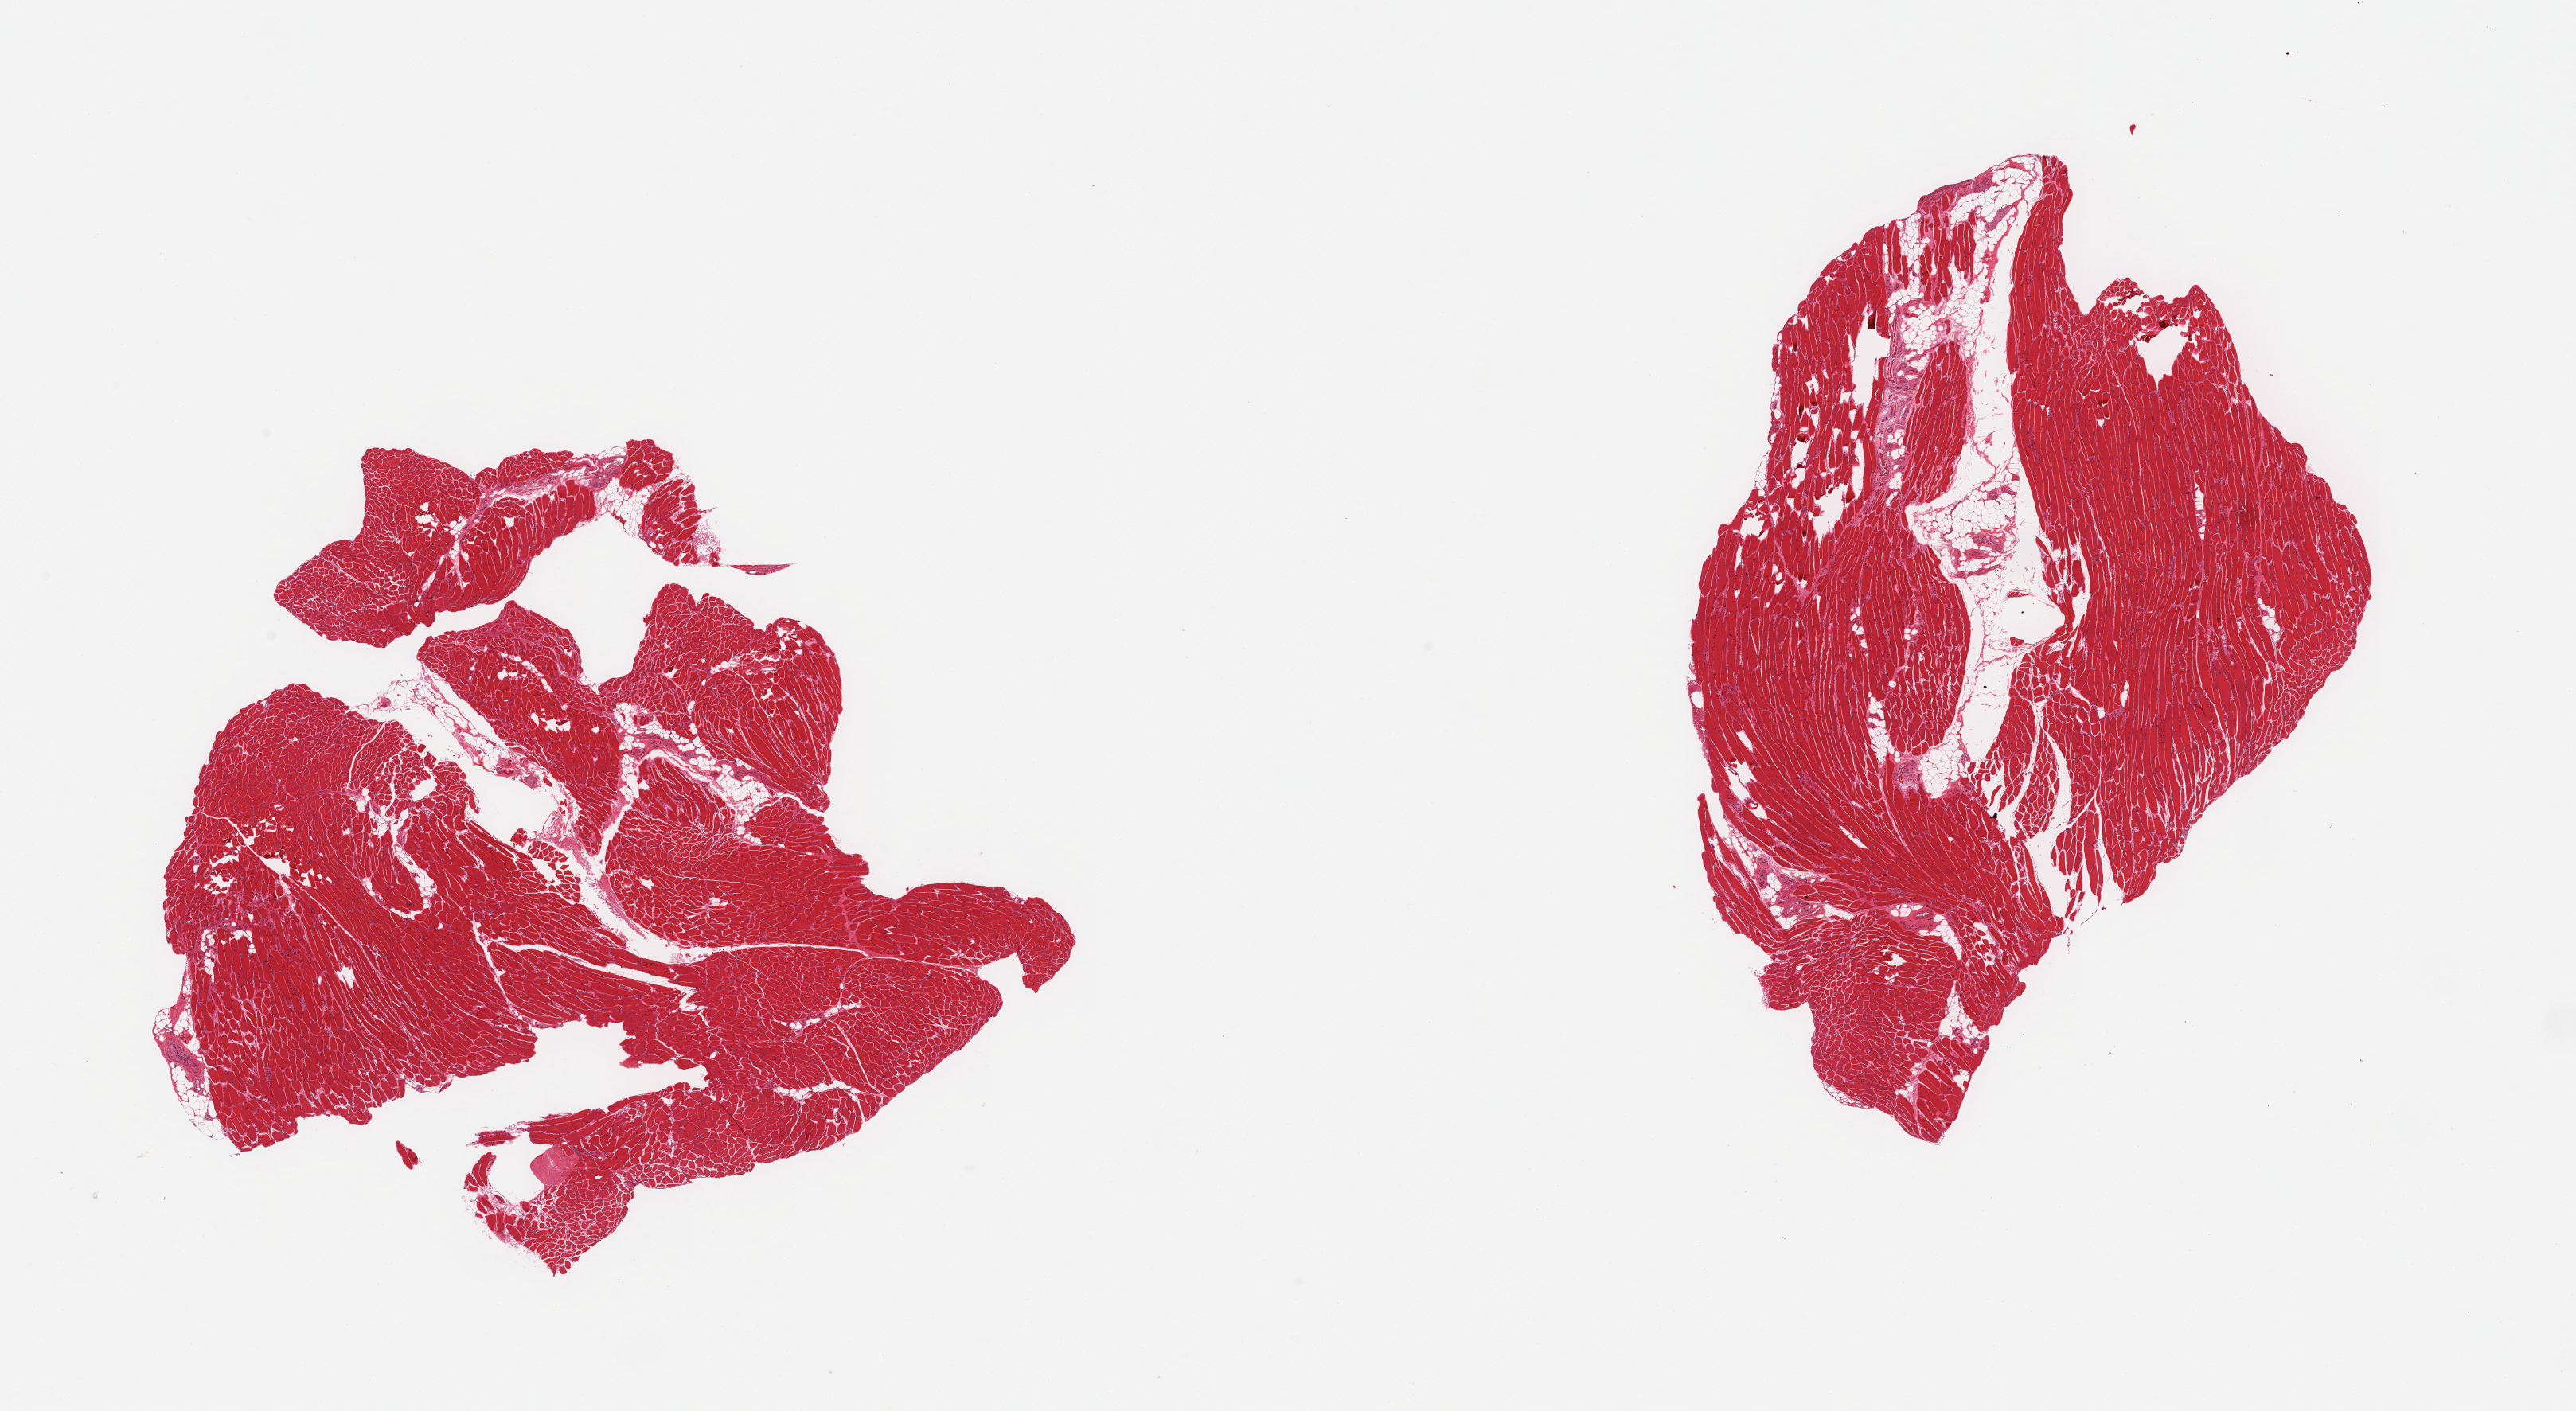
Hematoxylin and eosin (H&E) whole-slide image, a low-resolution overview of the entire scanned area, about 25.6 x 14.0 mm. PAXgene-fixed paraffin-embedded (PFPE) section. Target tissue: skeletal muscle. Tissue donor sample. Female donor.
Review note (as recorded): 2 pieces; minimal internal fat.